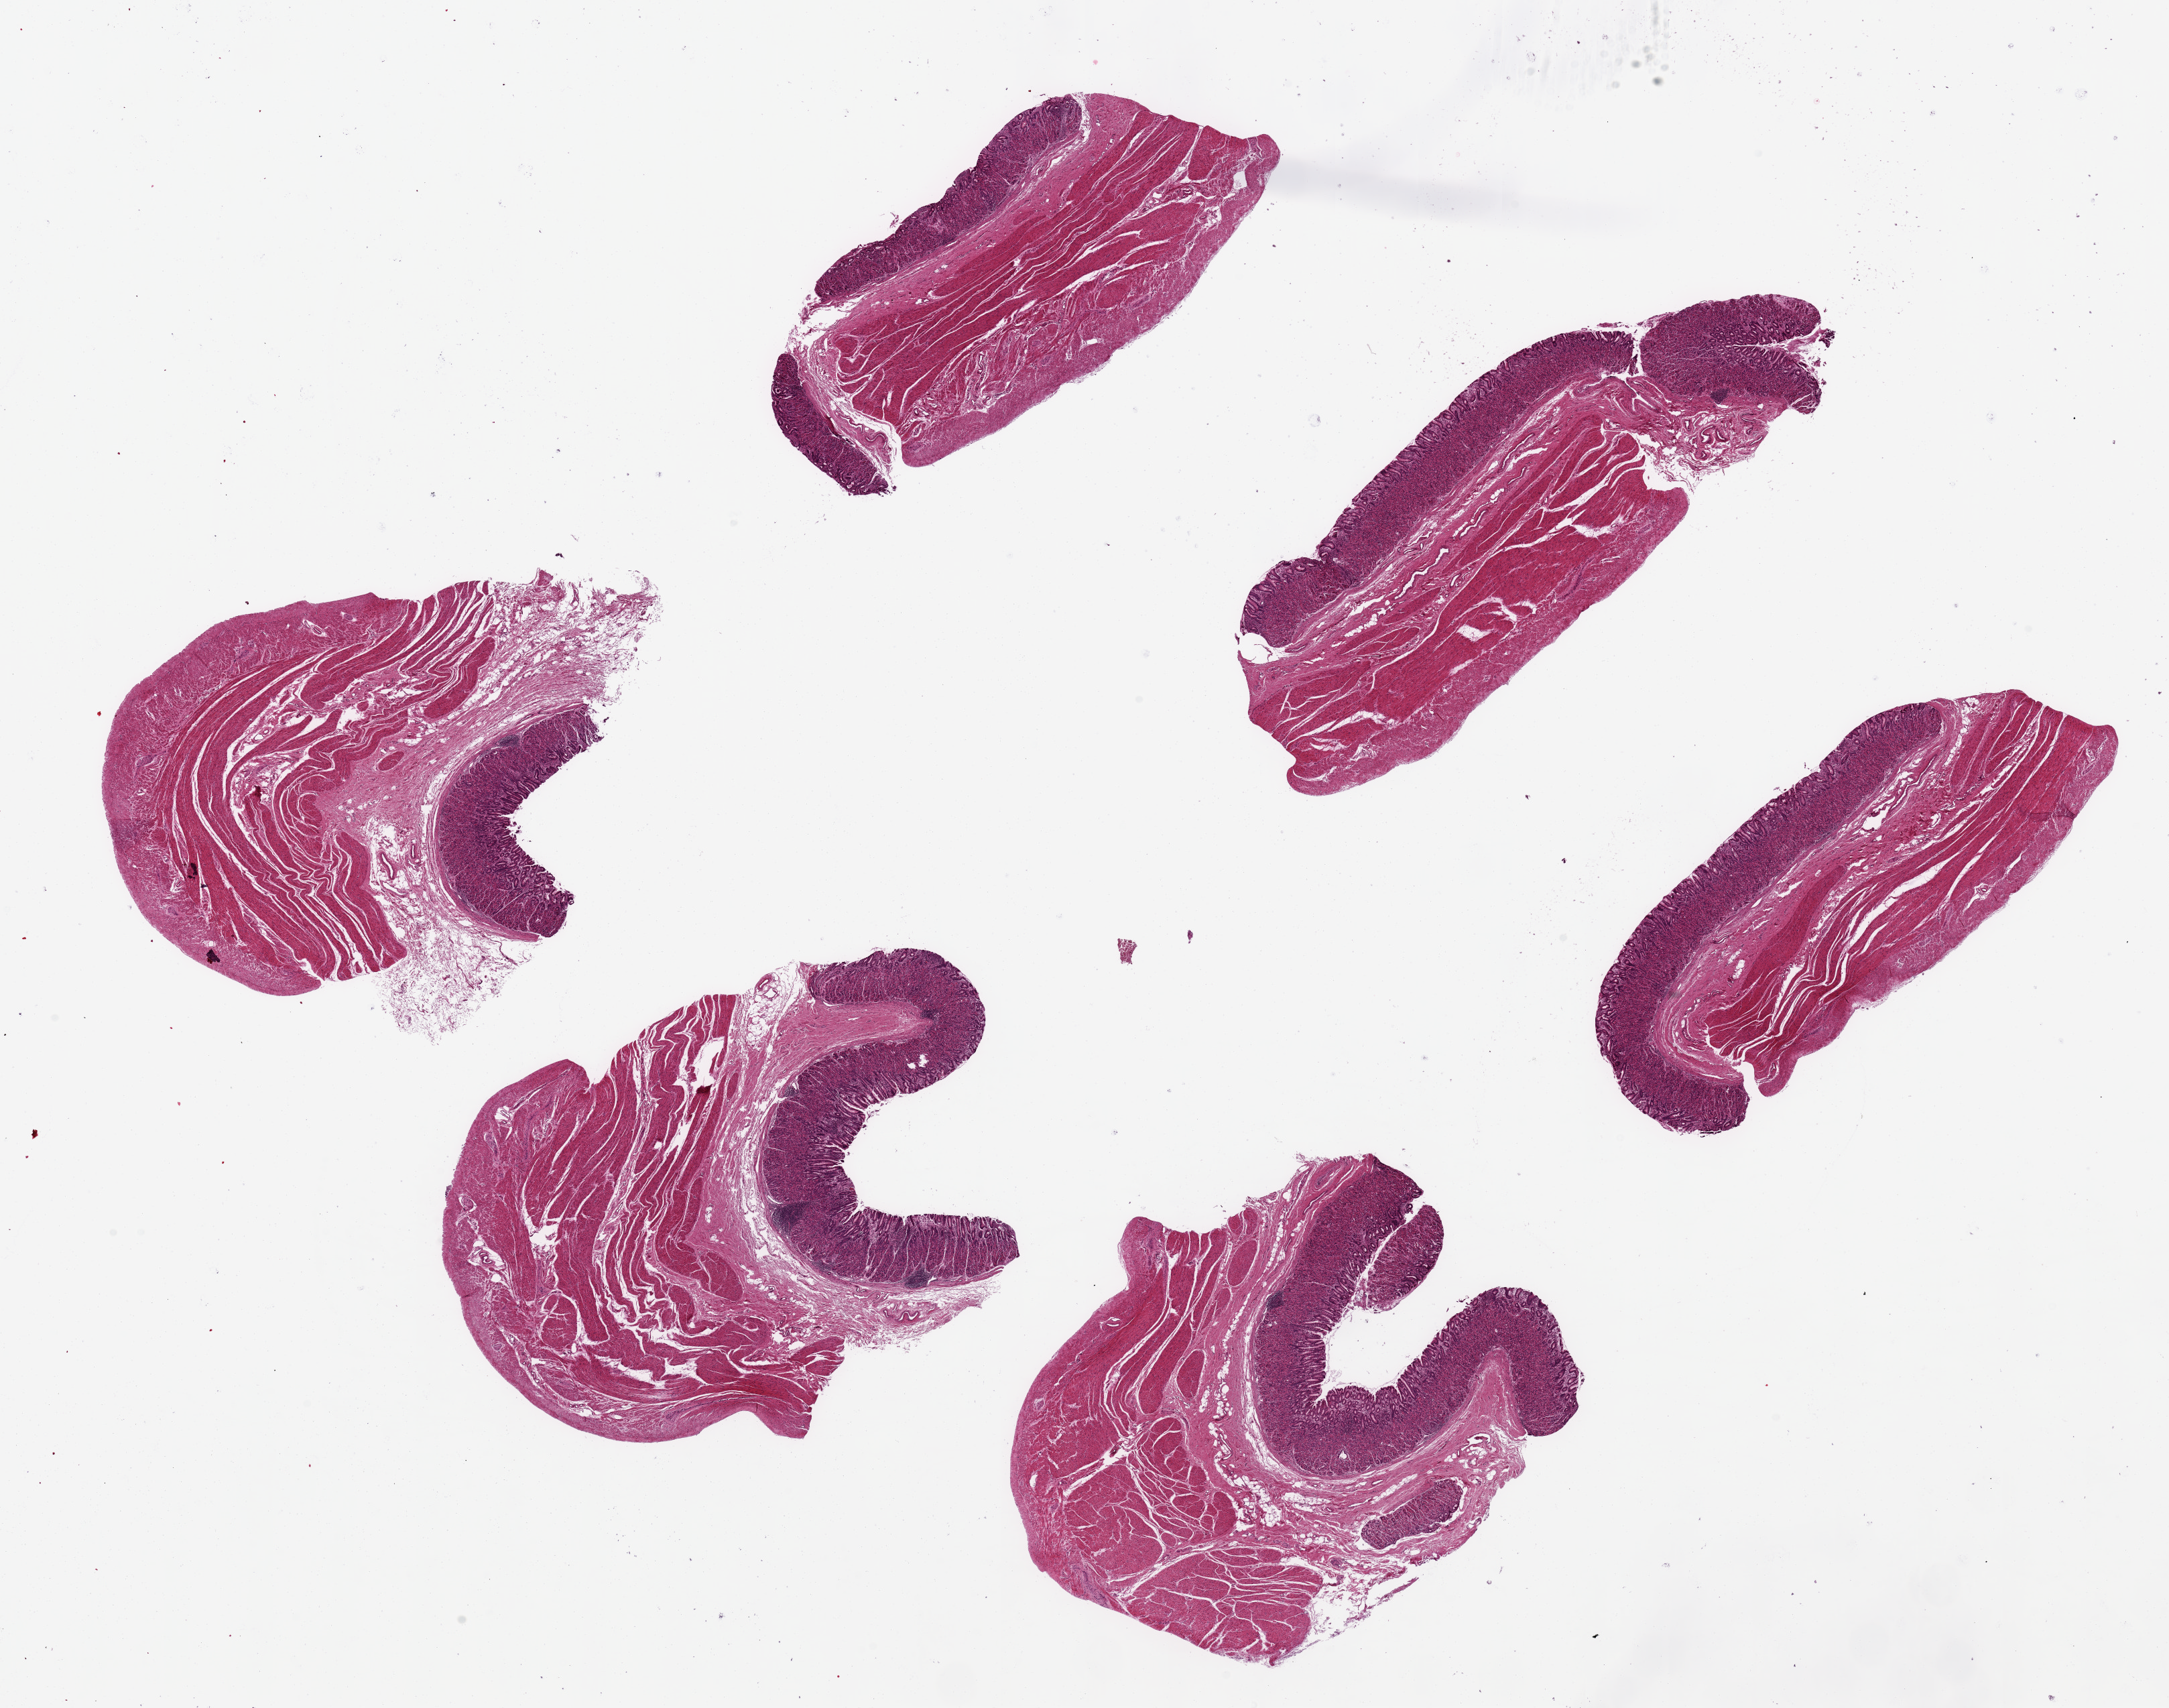
Whole-slide image, haematoxylin and eosin stain, brightfield — a low-resolution overview of the entire scanned area, about 25.6 x 20.2 mm, PAXgene-fixed, paraffin-embedded tissue, section of stomach (target tissue), donor tissue sample.
• pathologist's review note for this sample: 6 pieces, ~8x2.5mm, mucosa 0.8mm, mild chronic gastritis, well-preserved fundic mucosa